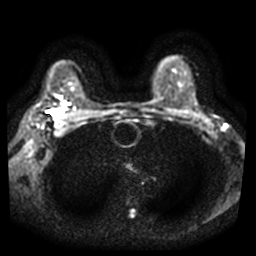
Breast MRI, one axial slice. Slice 25 of 37 in the series (ordered by position). Diffusion-weighted series; image 2 of 4 stored at this slice position (different b-values; order by instance number). 3 T. 256 × 256 image matrix, field of view 340 × 340 mm. Female patient.
Structures marked on this image (expert manual segmentation):
- tumour on diffusion-weighted imaging: box from (x=50, y=111) to (x=57, y=115) px